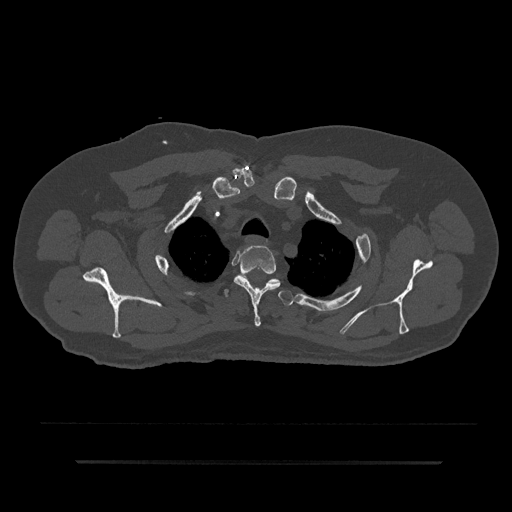
CT including the spine, one axial slice; slice 689 of 797 in the series (ordered by position); reconstruction kernel Br40s/3; bone window (W 1800 / L 400 HU); 512 × 512 image matrix, field of view 464 × 464 mm. Patient: male, 59 years. Case-level facts recorded for this patient, not image findings: primary cancer: bile ducts; vertebrae with lytic lesions (as recorded): T10.
Annotated regions visible in this slice (semi-automatic segmentation, software-assisted and operator-edited):
- T2 vertebra: bounding box (x1, y1, x2, y2) in pixels: (234, 246, 281, 327)
- T3 vertebra: (225, 289, 293, 306)